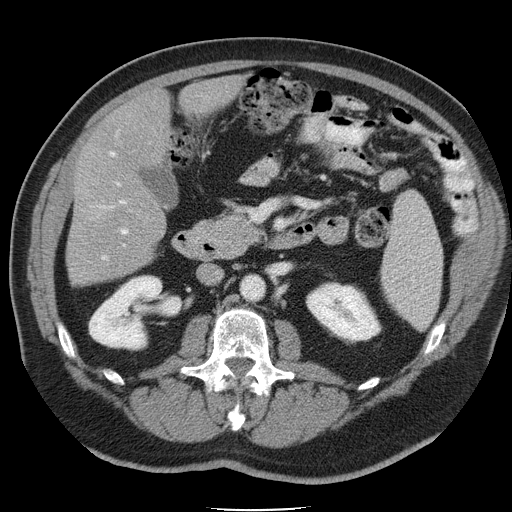
Contrast-enhanced abdominal CT, one axial slice. Slice 17 of 45 in the series (ordered by position). 120 kVp. Intravenous contrast given. Soft-tissue window (W 400 / L 40 HU). 5 mm slice thickness. 512 × 512 image matrix, field of view 386 × 386 mm. Male patient, age 65 years. From the clinical record (not read from this slice): diagnosis: colorectal cancer liver metastases, imaged before liver resection.
Outlined on this slice (expert manual segmentation):
- hepatic veins: bounding box <101,152,115,260> (left, top, right, bottom; pixels)
- liver: <67,79,239,284>
- planned liver remnant (the part of the liver to remain after resection): <93,79,239,172>
- portal vein (with intrahepatic branches): <117,183,128,234>